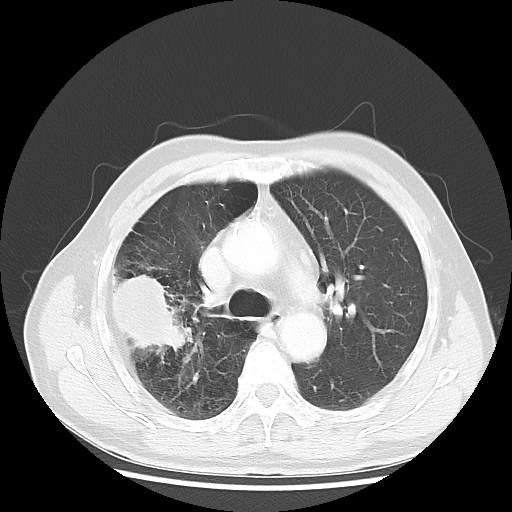
Chest CT, one axial slice. Position 33 of 50 along the scan axis. 120 kVp. Lung window (W 1500 / L -600 HU). 5 mm slice thickness. 512 × 512 image matrix. Patient: male, 69 years. Case-level facts recorded for this patient, not image findings: clinical TNM (as recorded): T3 N0 M0; histopathological grade: G3.
Annotated regions visible in this slice (rectangle marked by the reading radiologist):
- lung tumour (recorded histology: adenocarcinoma): bounding box [x1, y1, x2, y2] px = [106, 271, 195, 351]